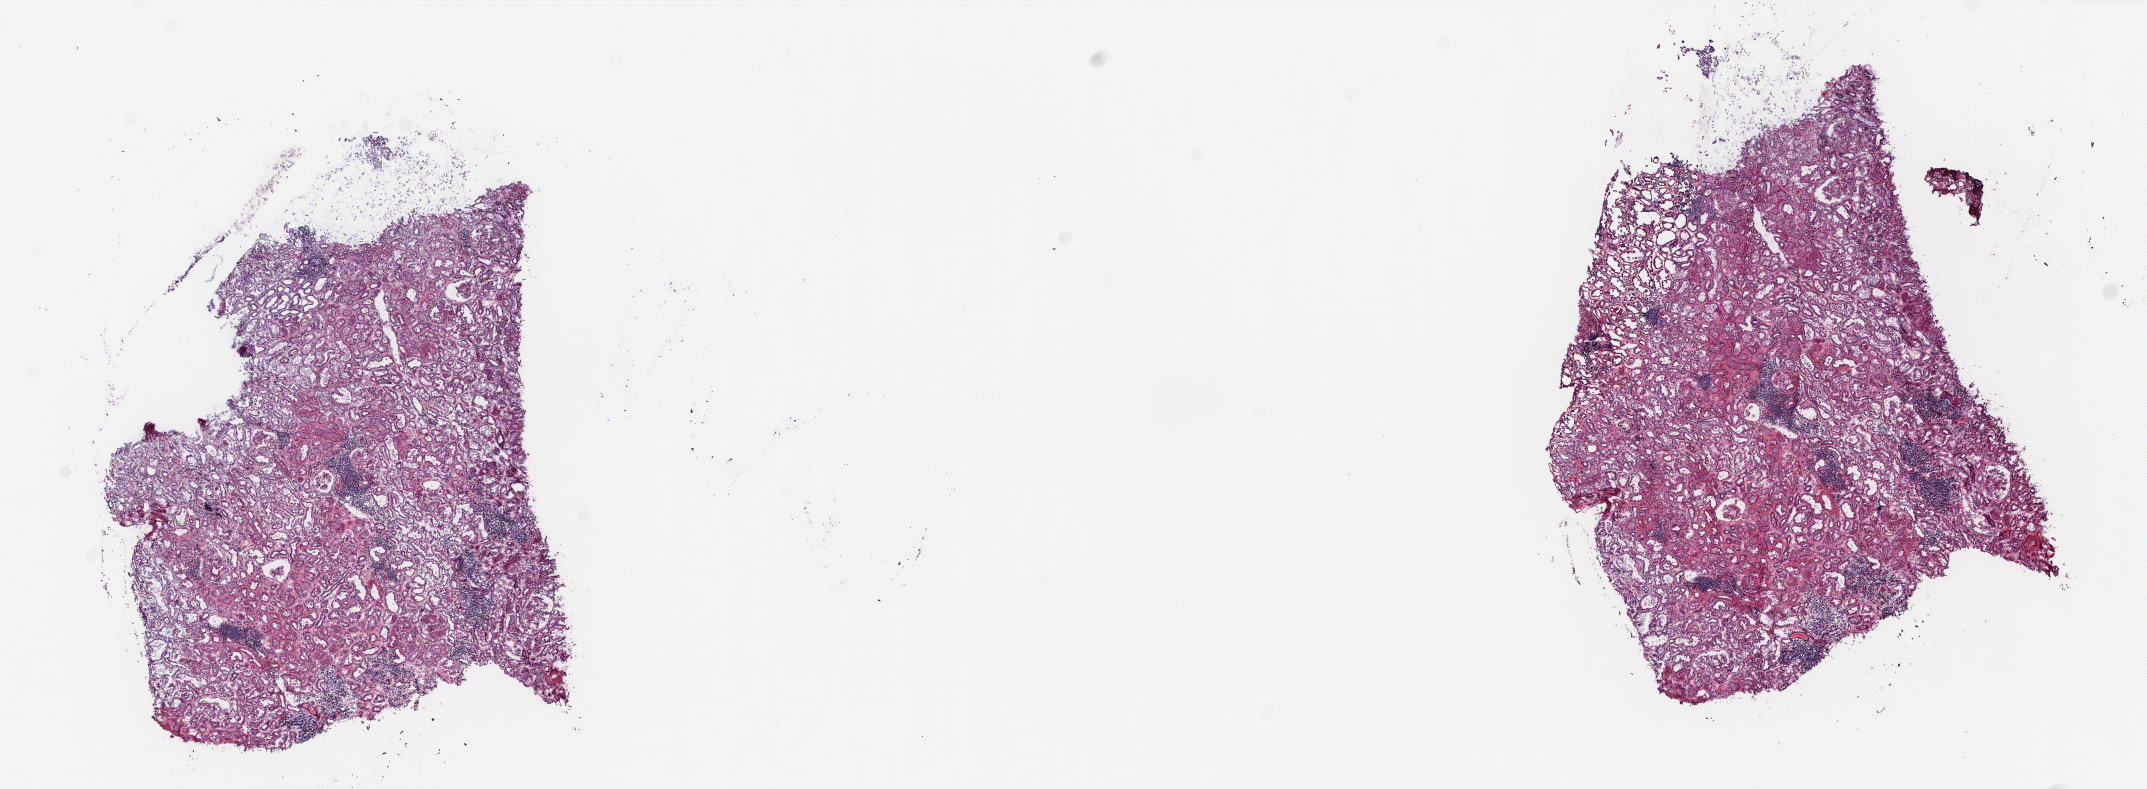
Whole-slide histology image, H&E-stained, shown as a low-resolution overview of the whole scanned area (about 17.3 x 6.4 mm). Frozen section from the top of the tissue portion. Kidney, solid tissue normal (non-tumour tissue) sample. Male, age 75 years at initial diagnosis. Slide review estimates, as recorded: tumour cells 0%, tumour nuclei 0%, normal cells 100%, stromal cells 0%, necrosis 0%. Infiltration values recorded for this section: lymphocyte infiltration 6%, monocyte infiltration 0%, neutrophil infiltration 0%.
• this section: solid tissue normal (non-tumour) sample from the same patient
• patient diagnosis: Papillary adenocarcinoma, NOS